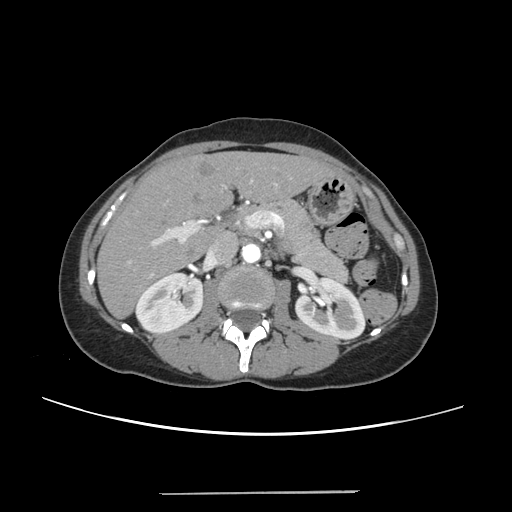
Contrast-enhanced abdominal CT, one axial slice. Position 126 of 240 along the scan axis. Intravenous contrast given. Soft-tissue window (W 400 / L 40 HU). 1.25 mm slice thickness. 512 × 512 image matrix. Female patient, age 60 years. From the clinical record (not read from this slice): diagnosis: colorectal cancer liver metastases, imaged before liver resection; multiple liver metastases: no; largest metastasis: 1.5 cm; disease in both lobes: no.
Outlined on this slice (manually delineated by an expert):
- liver: bounding box <99,152,331,316> (left, top, right, bottom; pixels)
- planned liver remnant (the part of the liver to remain after resection): <99,153,331,317>
- portal vein (with intrahepatic branches): <127,179,278,275>
- liver metastasis: <199,162,218,177>